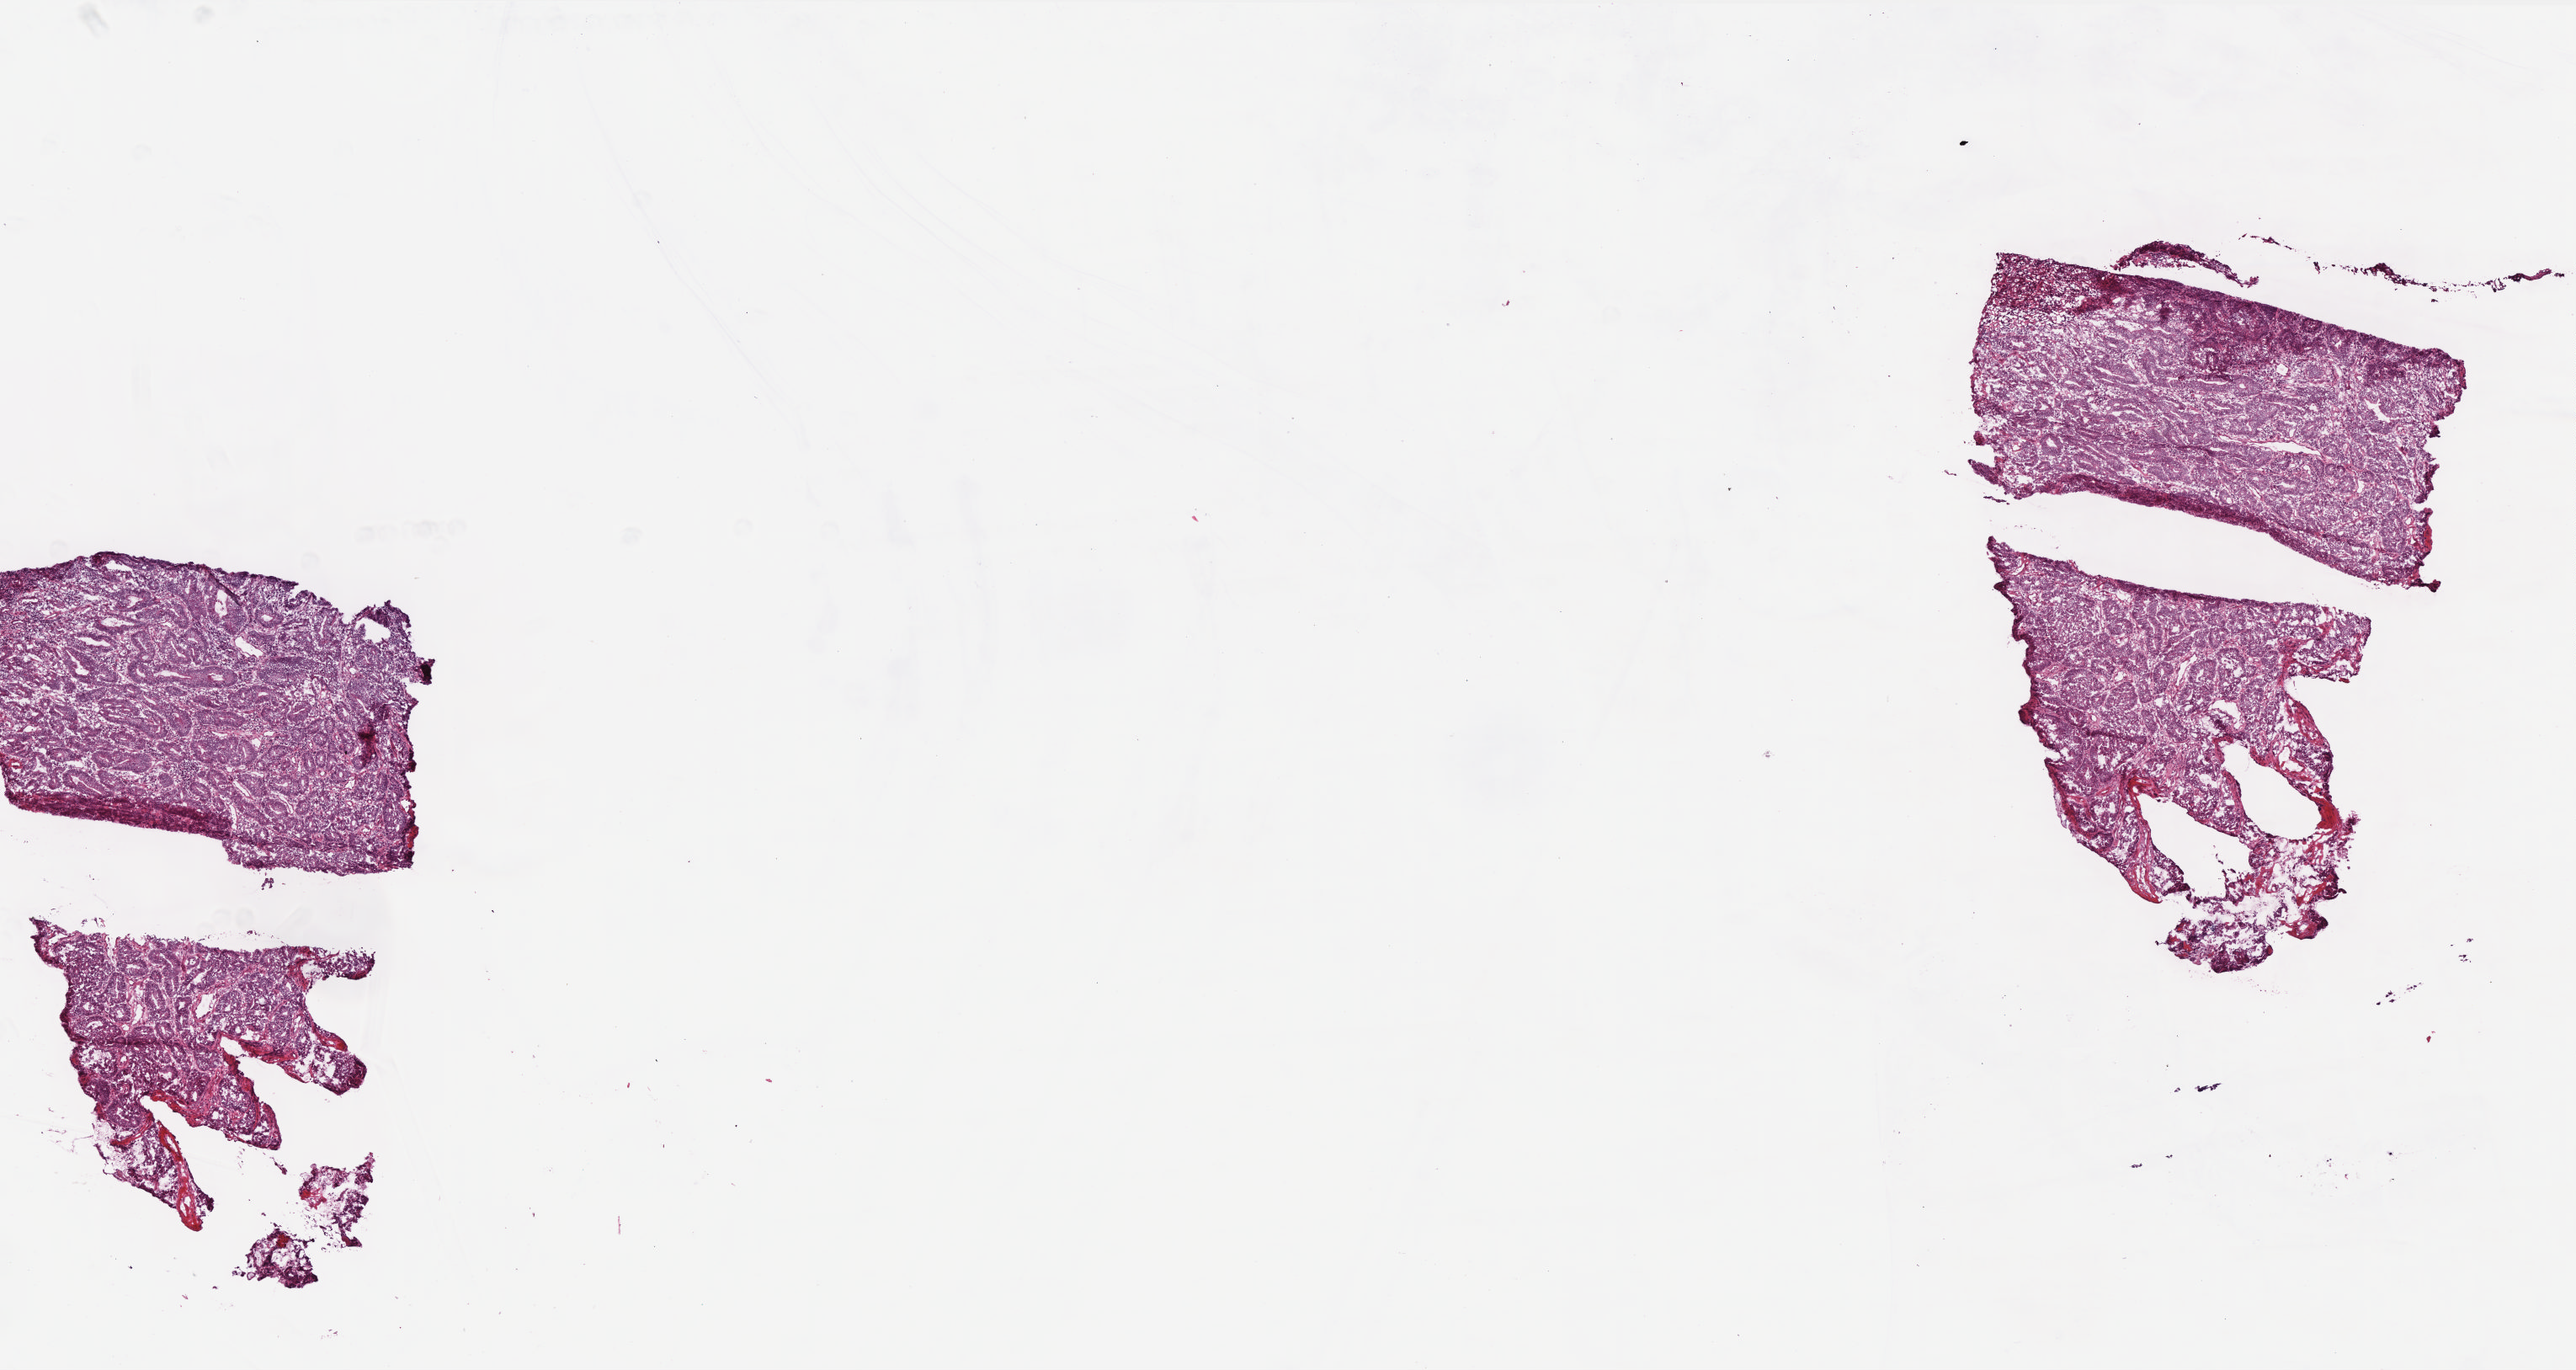
Digitized Hematoxylin and eosin (H&E) stained tissue section (whole slide) — low-resolution overview of the scanned area, about 12.3 x 6.5 mm; frozen section from the top of the tissue portion; primary tumour sample from the colon. Male patient; age at initial diagnosis 80 years. Slide review estimates, as recorded: tumour cells 95%, tumour nuclei 90%, normal cells 0%, stromal cells 4%, necrosis 1%. Inflammatory infiltration, as recorded: lymphocyte infiltration 3%, monocyte infiltration 1%, neutrophil infiltration 0%.
Pathologic diagnosis: Adenocarcinoma, NOS (ascending colon). AJCC pathologic stage: IIA (6th edition).